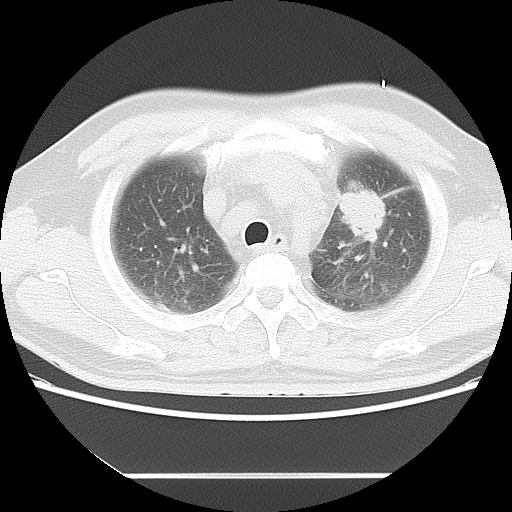
Chest CT, one axial slice. Slice 9 of 14 in the series (ordered by position). Reconstruction kernel LUNG. Lung window (W 1500 / L -600 HU). 5 mm slice thickness. 512 × 512 image matrix, field of view 350 × 350 mm. Male patient, age 56 years. From the clinical record (not read from this slice): clinical TNM (as recorded): T2 N3 M1.
Annotated regions visible in this slice (bounding box drawn by a radiologist):
- lung tumour (recorded histology: adenocarcinoma): box from (x=331, y=176) to (x=388, y=252) px